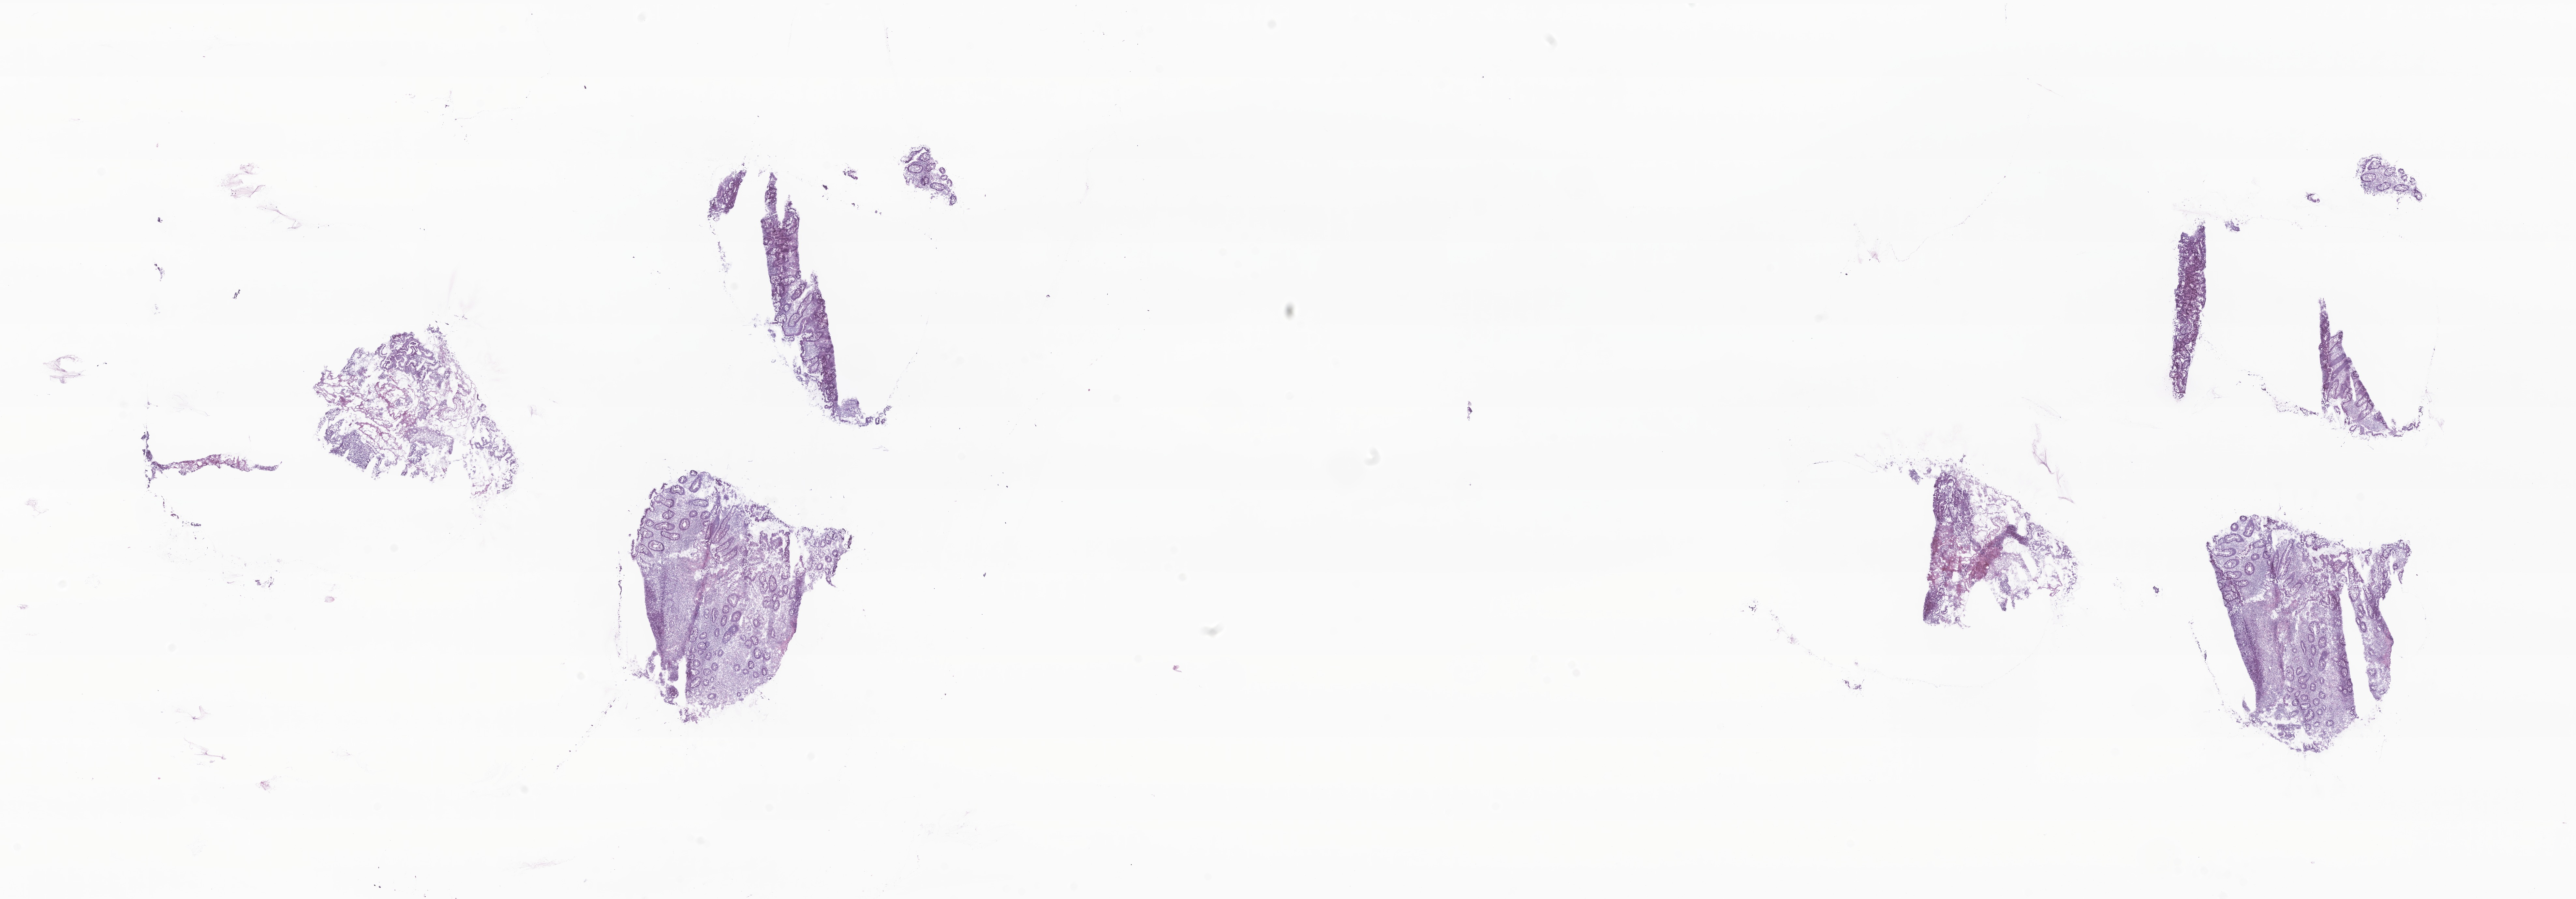
Digitized hematoxylin and eosin (H&E)-stained section, a low-resolution overview of the entire scanned area, about 33.3 x 11.6 mm. Frozen section. Specimen: primary tumor. Site: cecum. Female, age 82 years at initial diagnosis. Pathologist review of this section (percent, as recorded): tumor cells 15%, tumor nuclei 50%, stromal cells 60%, necrosis 1%, normal cells 24%. Inflammatory infiltration, as recorded: lymphocyte infiltration 32%, monocyte infiltration 2%, neutrophil infiltration 0%.
• section: top of the tissue portion
• histologic diagnosis: Adenocarcinoma, NOS